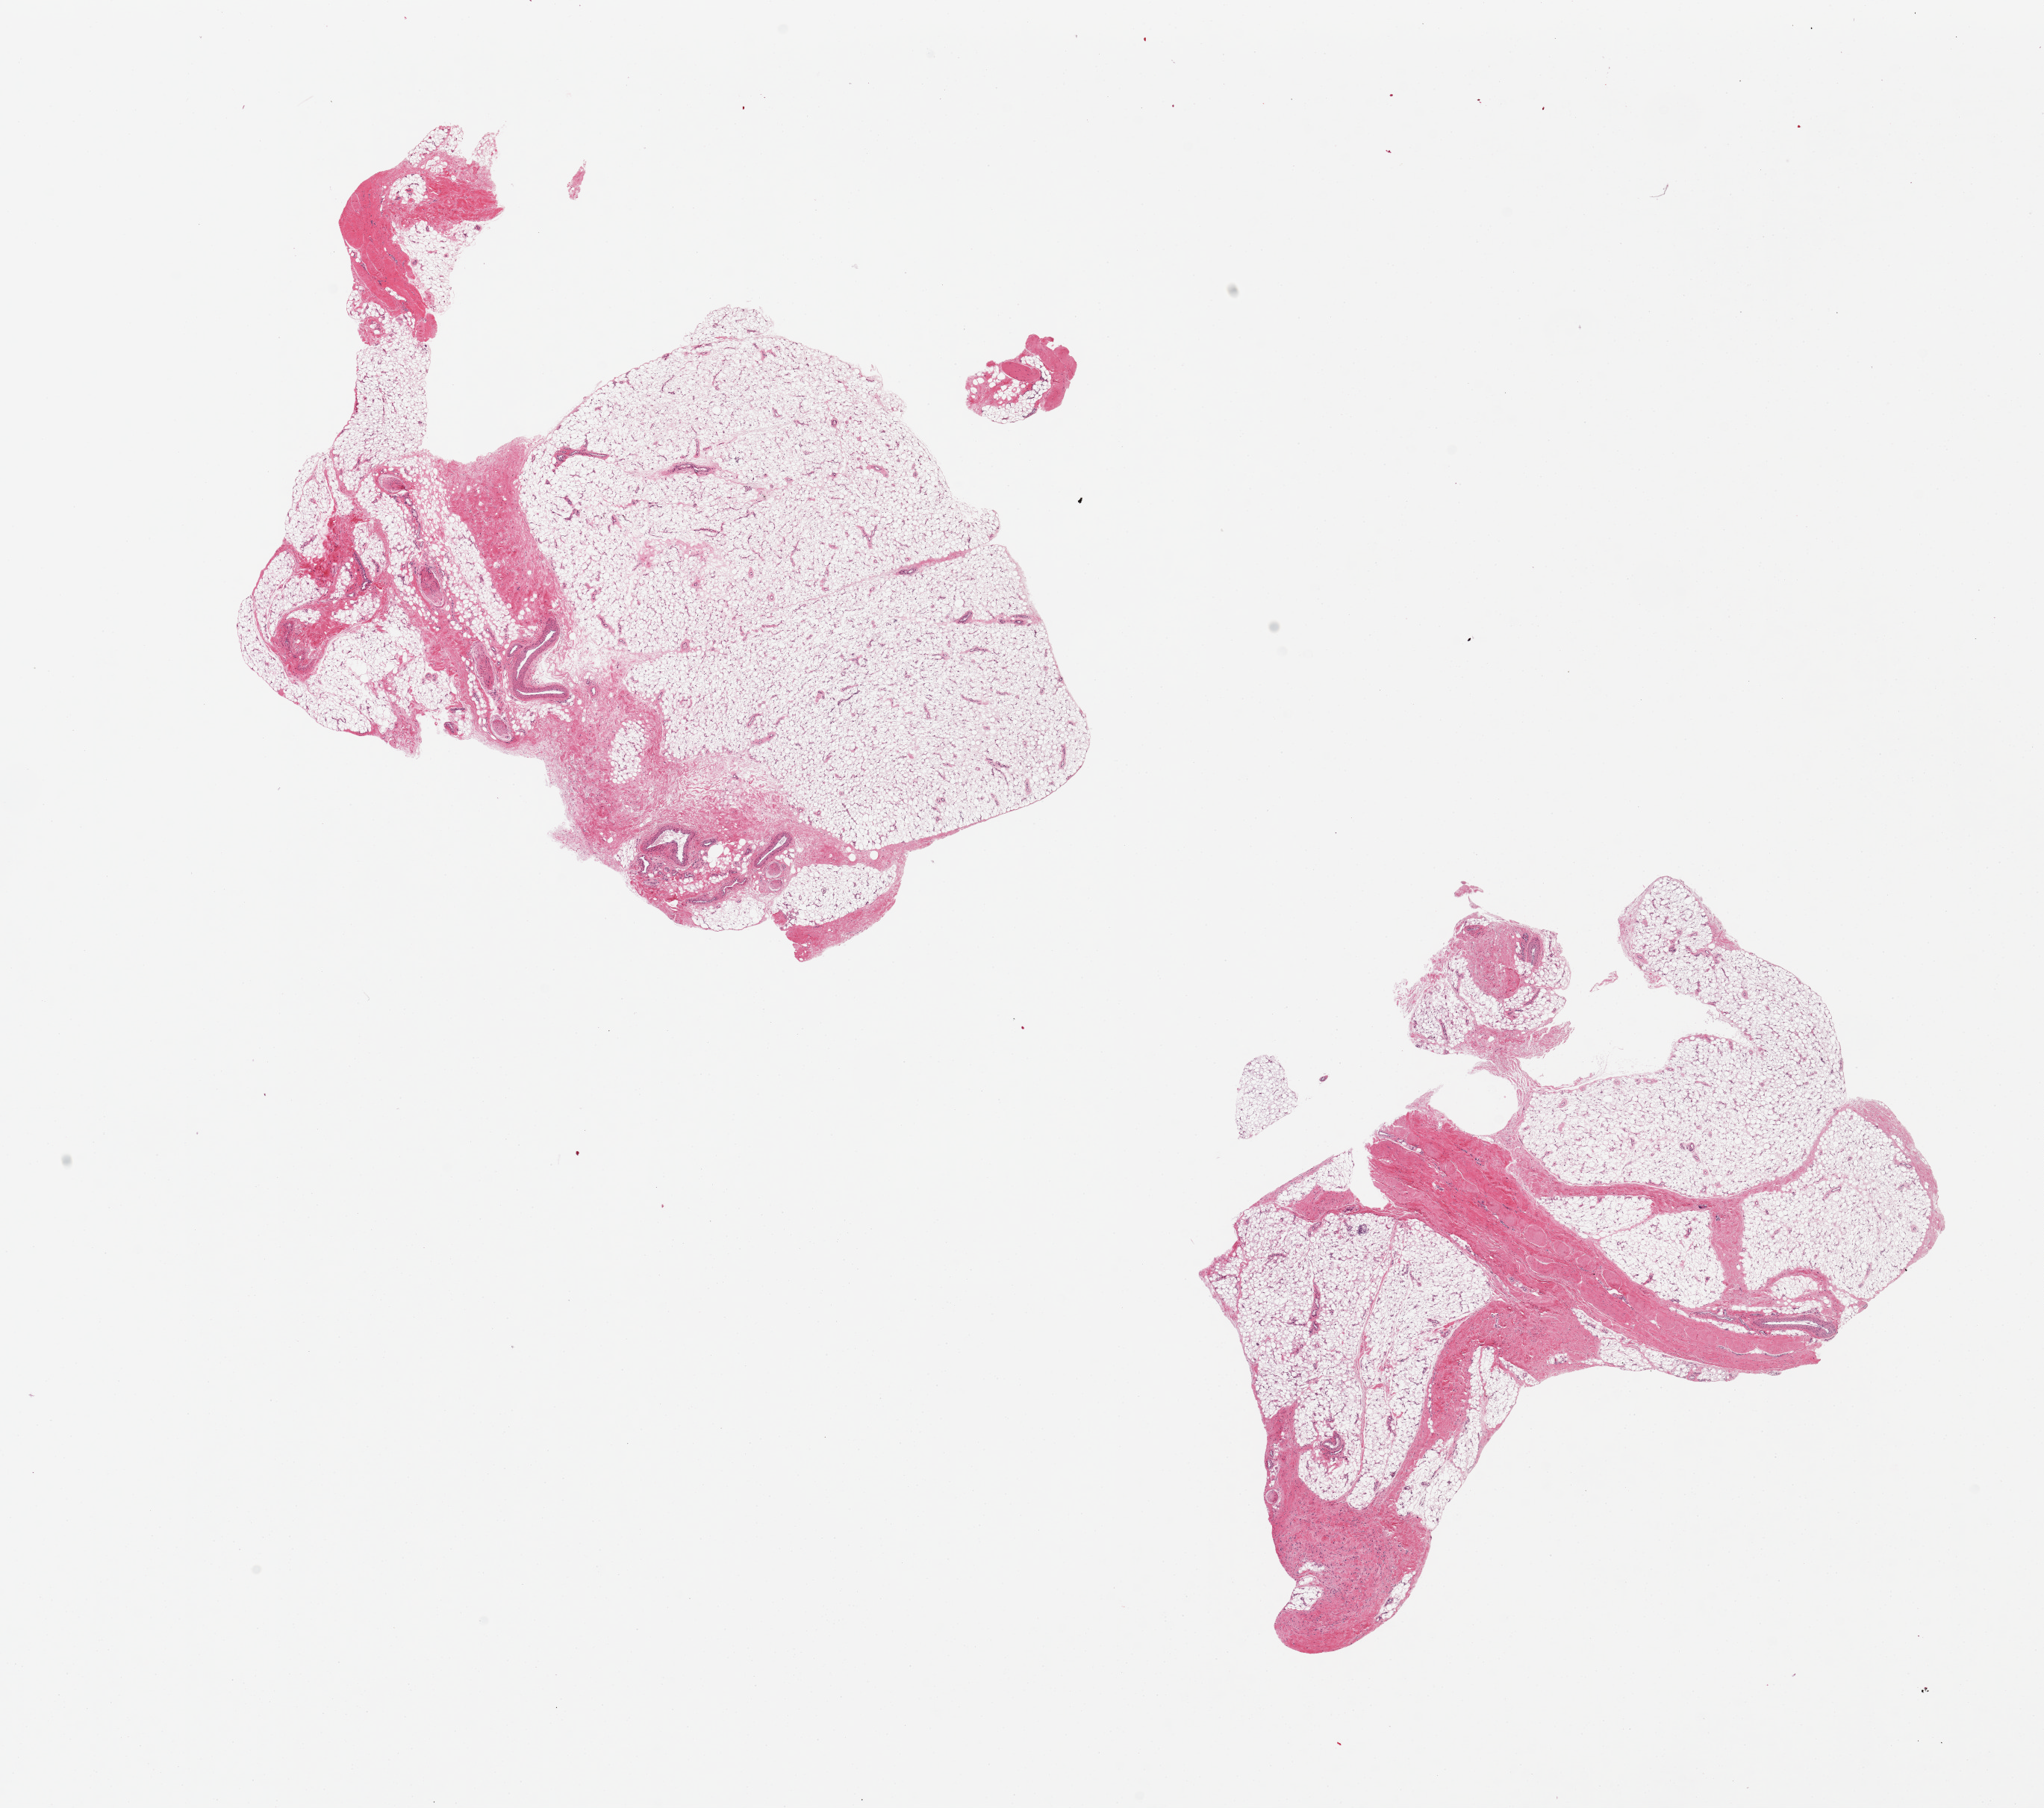
Whole-slide image, haematoxylin and eosin stain, brightfield — low-resolution overview of the scanned area, about 21.7 x 19.2 mm; PAXgene-fixed paraffin-embedded (PFPE) section; target tissue: adipose tissue; tissue donor sample. Donor: male.
Reviewer comment on this tissue sample: 2 pieces; approximately 20% fibrovascular tissue and nerve present.